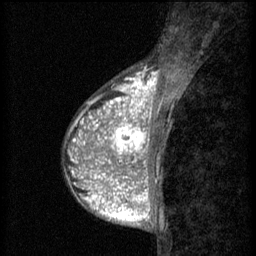
Breast MRI (dynamic contrast-enhanced), one sagittal slice. Position 22 of 60 along the scan axis. 3 images stored at this slice position (order not interpretable as contrast timing). 1.5 T. TE 4.2 ms, TR 8.2 ms. 2 mm slice thickness. 256 × 256 image matrix, field of view 180 × 180 mm. Female patient, age 38 years.
Structures marked on this image (semi-automatically segmented with operator editing):
- analysis volume of interest (the breast-tissue region the enhancement analysis was run in; not a lesion): bounding box <92,112,152,171> (left, top, right, bottom; pixels)
- tumour enhancement mask (voxels above the 70 % enhancement threshold inside the analysis volume of interest): <92,112,152,171>